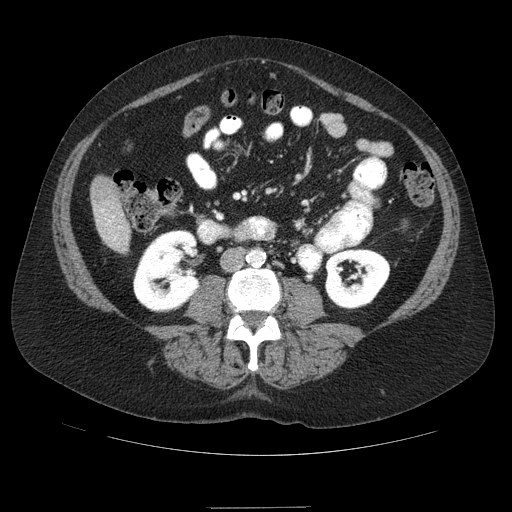
Contrast-enhanced abdominal CT (liver protocol), one axial slice; slice 15 of 89 in the series (ordered by position); reconstruction kernel STANDARD; 120 kVp; soft-tissue window (W 400 / L 40 HU); 2.5 mm slice thickness; 512 × 512 image matrix, field of view 400 × 400 mm. From the clinical record (not read from this slice): diagnosis: hepatocellular carcinoma (patient treated with transarterial chemoembolisation; whether this scan precedes or follows treatment is not stated here); TNM stage (as recorded): Stage-IIIB; Child-Pugh class: A; tumour nodularity: multinodular.
Outlined on this slice (semi-automatically segmented with operator editing):
- liver parenchyma outside the tumour (the mass and vessels are separate outlines, so this box may not span the whole liver): bounding box <90,176,130,252> (left, top, right, bottom; pixels)
- liver vessels: <101,209,116,239>